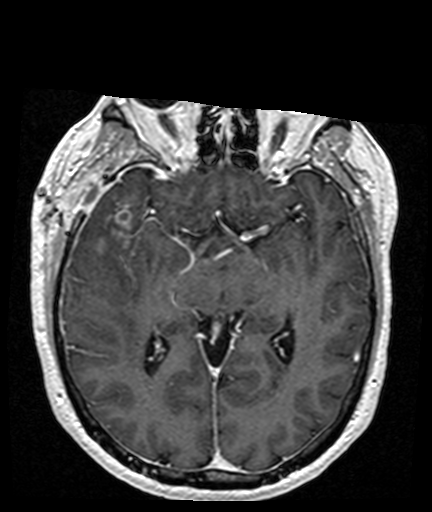
Brain MRI from a brain-tumour surgery series, one axial slice; position 95 of 176 along the scan axis; T1-weighted post-contrast; 432 × 512 image matrix, field of view 194 × 230 mm. From the clinical record (not read from this slice): histopathology: Glioblastoma; WHO grade: 4; IDH mutation: no; tumour location: Right Frontal Temporal, Posterior Sylvian Fissure.
Annotated regions visible in this slice (expert manual segmentation):
- tumour: box from (x=100, y=208) to (x=134, y=254) px